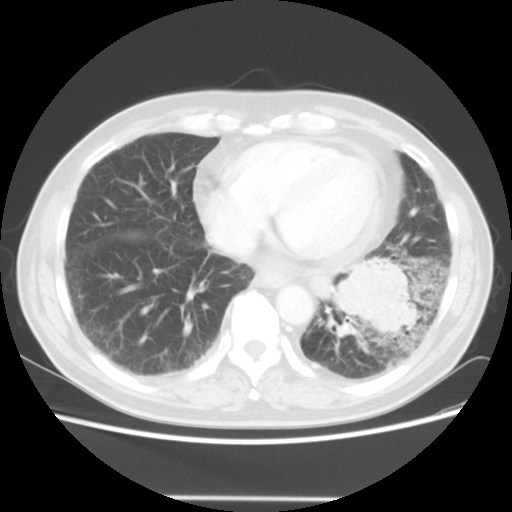
Chest CT, one axial slice; position 15 of 56 along the scan axis; reconstruction kernel STANDARD; 140 kVp; lung window (W 1500 / L -600 HU); 5 mm slice thickness; 512 × 512 image matrix, field of view 360 × 360 mm. Male patient, age 66 years. Case-level facts recorded for this patient, not image findings: clinical TNM (as recorded): T4 N3 M0.
Structures marked on this image (rectangle marked by the reading radiologist):
- lung tumour (recorded histology: small cell carcinoma): box from (x=328, y=249) to (x=428, y=350) px